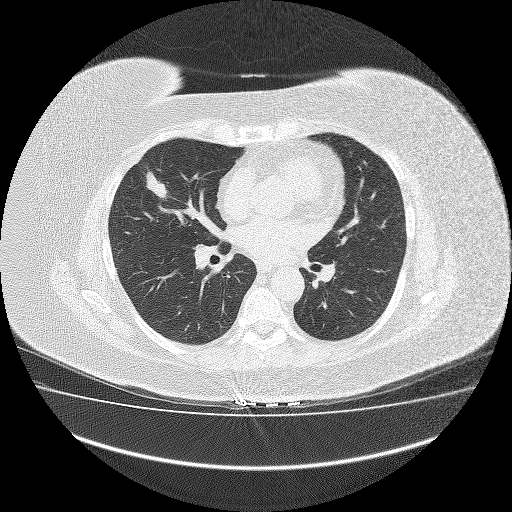
Axial slice from a low-dose chest CT screening exam, third annual screen, lung window (W 1500 / L -600 HU), lung (sharp) reconstruction kernel (FC51). Female participant, aged 64 years at enrolment. Former smoker at enrolment.
Lesion marked by an expert reader, bounding box (x1, y1, x2, y2) in pixels: (131, 167, 182, 211). The exam's reader record, not a measurement of the box and not confirmed to be the same lesion: non-calcified nodule or mass ≥4 mm, right middle lobe, 23 × 13 mm, smooth margins, soft tissue attenuation, pre-existing on the prior screen: no. Official screen result: positive, other.